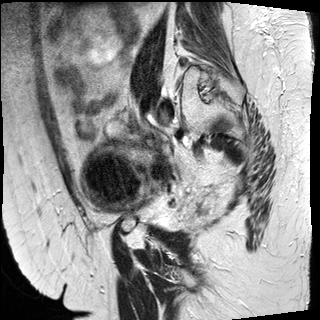
Pelvic MRI for cervical cancer, one sagittal slice. Position 17 of 50 along the scan axis. T2-weighted. 1.5 T. TE 89 ms, TR 4880 ms. 320 × 320 image matrix. Patient: female, 50 years.
Structures marked on this image (expert manual segmentation):
- uterus and cervix: bounding box <80,137,173,214> (left, top, right, bottom; pixels)